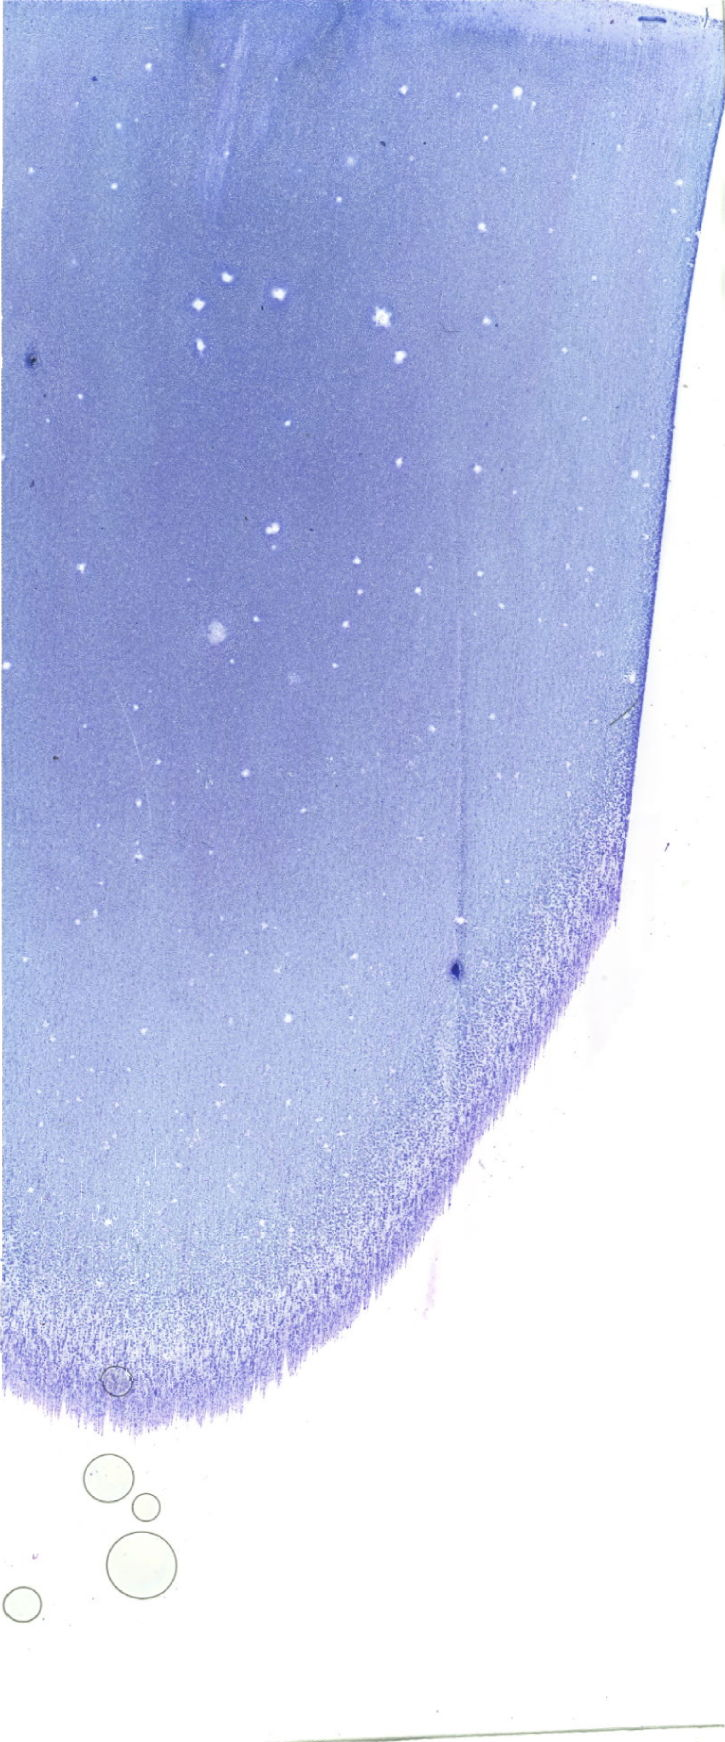
Bone marrow aspirate smear, May-Grünwald-Giemsa (MGG) stain, whole-slide image — low-resolution overview of the scanned area, about 20.6 x 49.4 mm. Patient sex: female.
Diagnosis: Acute Myelomonocytic Leukemia with Abnormal Eosinophils.